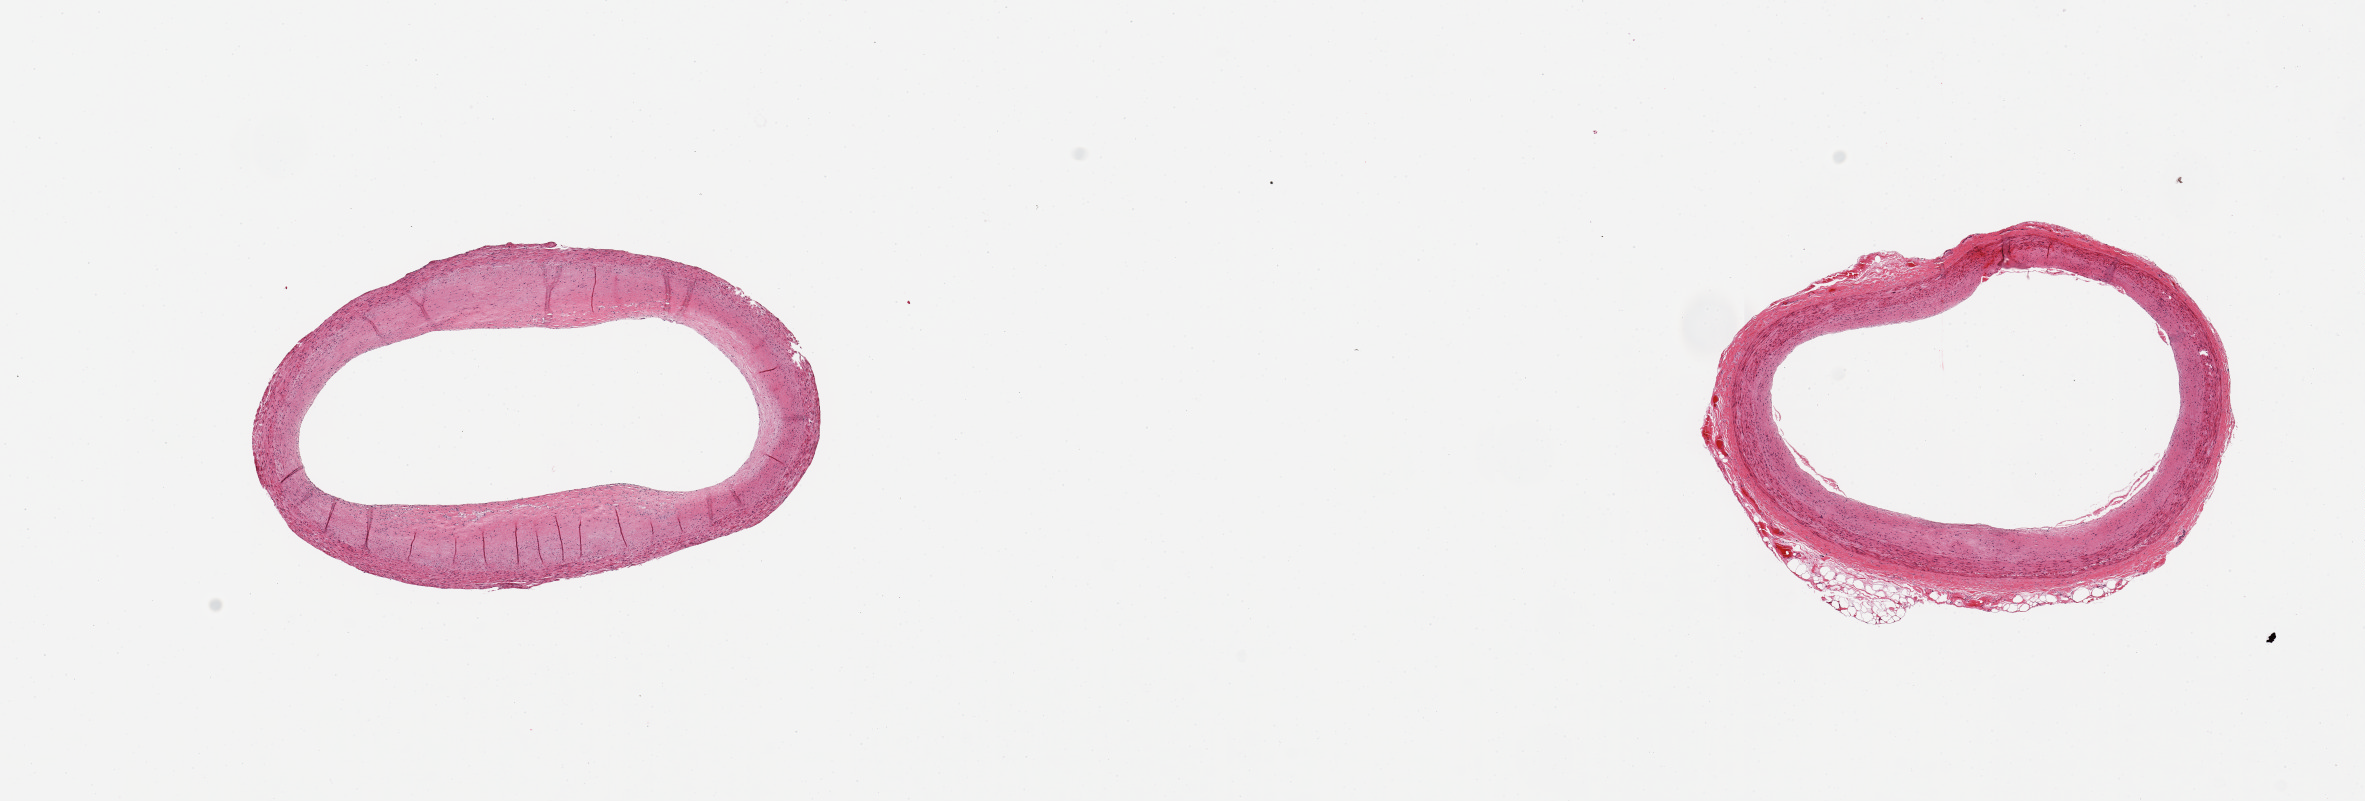
H&E whole-slide image — whole scanned area (about 18.7 x 6.3 mm) shown as a low-resolution overview. PAXgene-fixed paraffin-embedded (PFPE) section. Sampled site (target tissue): coronary artery. Tissue donor sample. Male donor.
• pathologist's review note for this sample: 2 pieces; mild intimall thickening; well trimmed